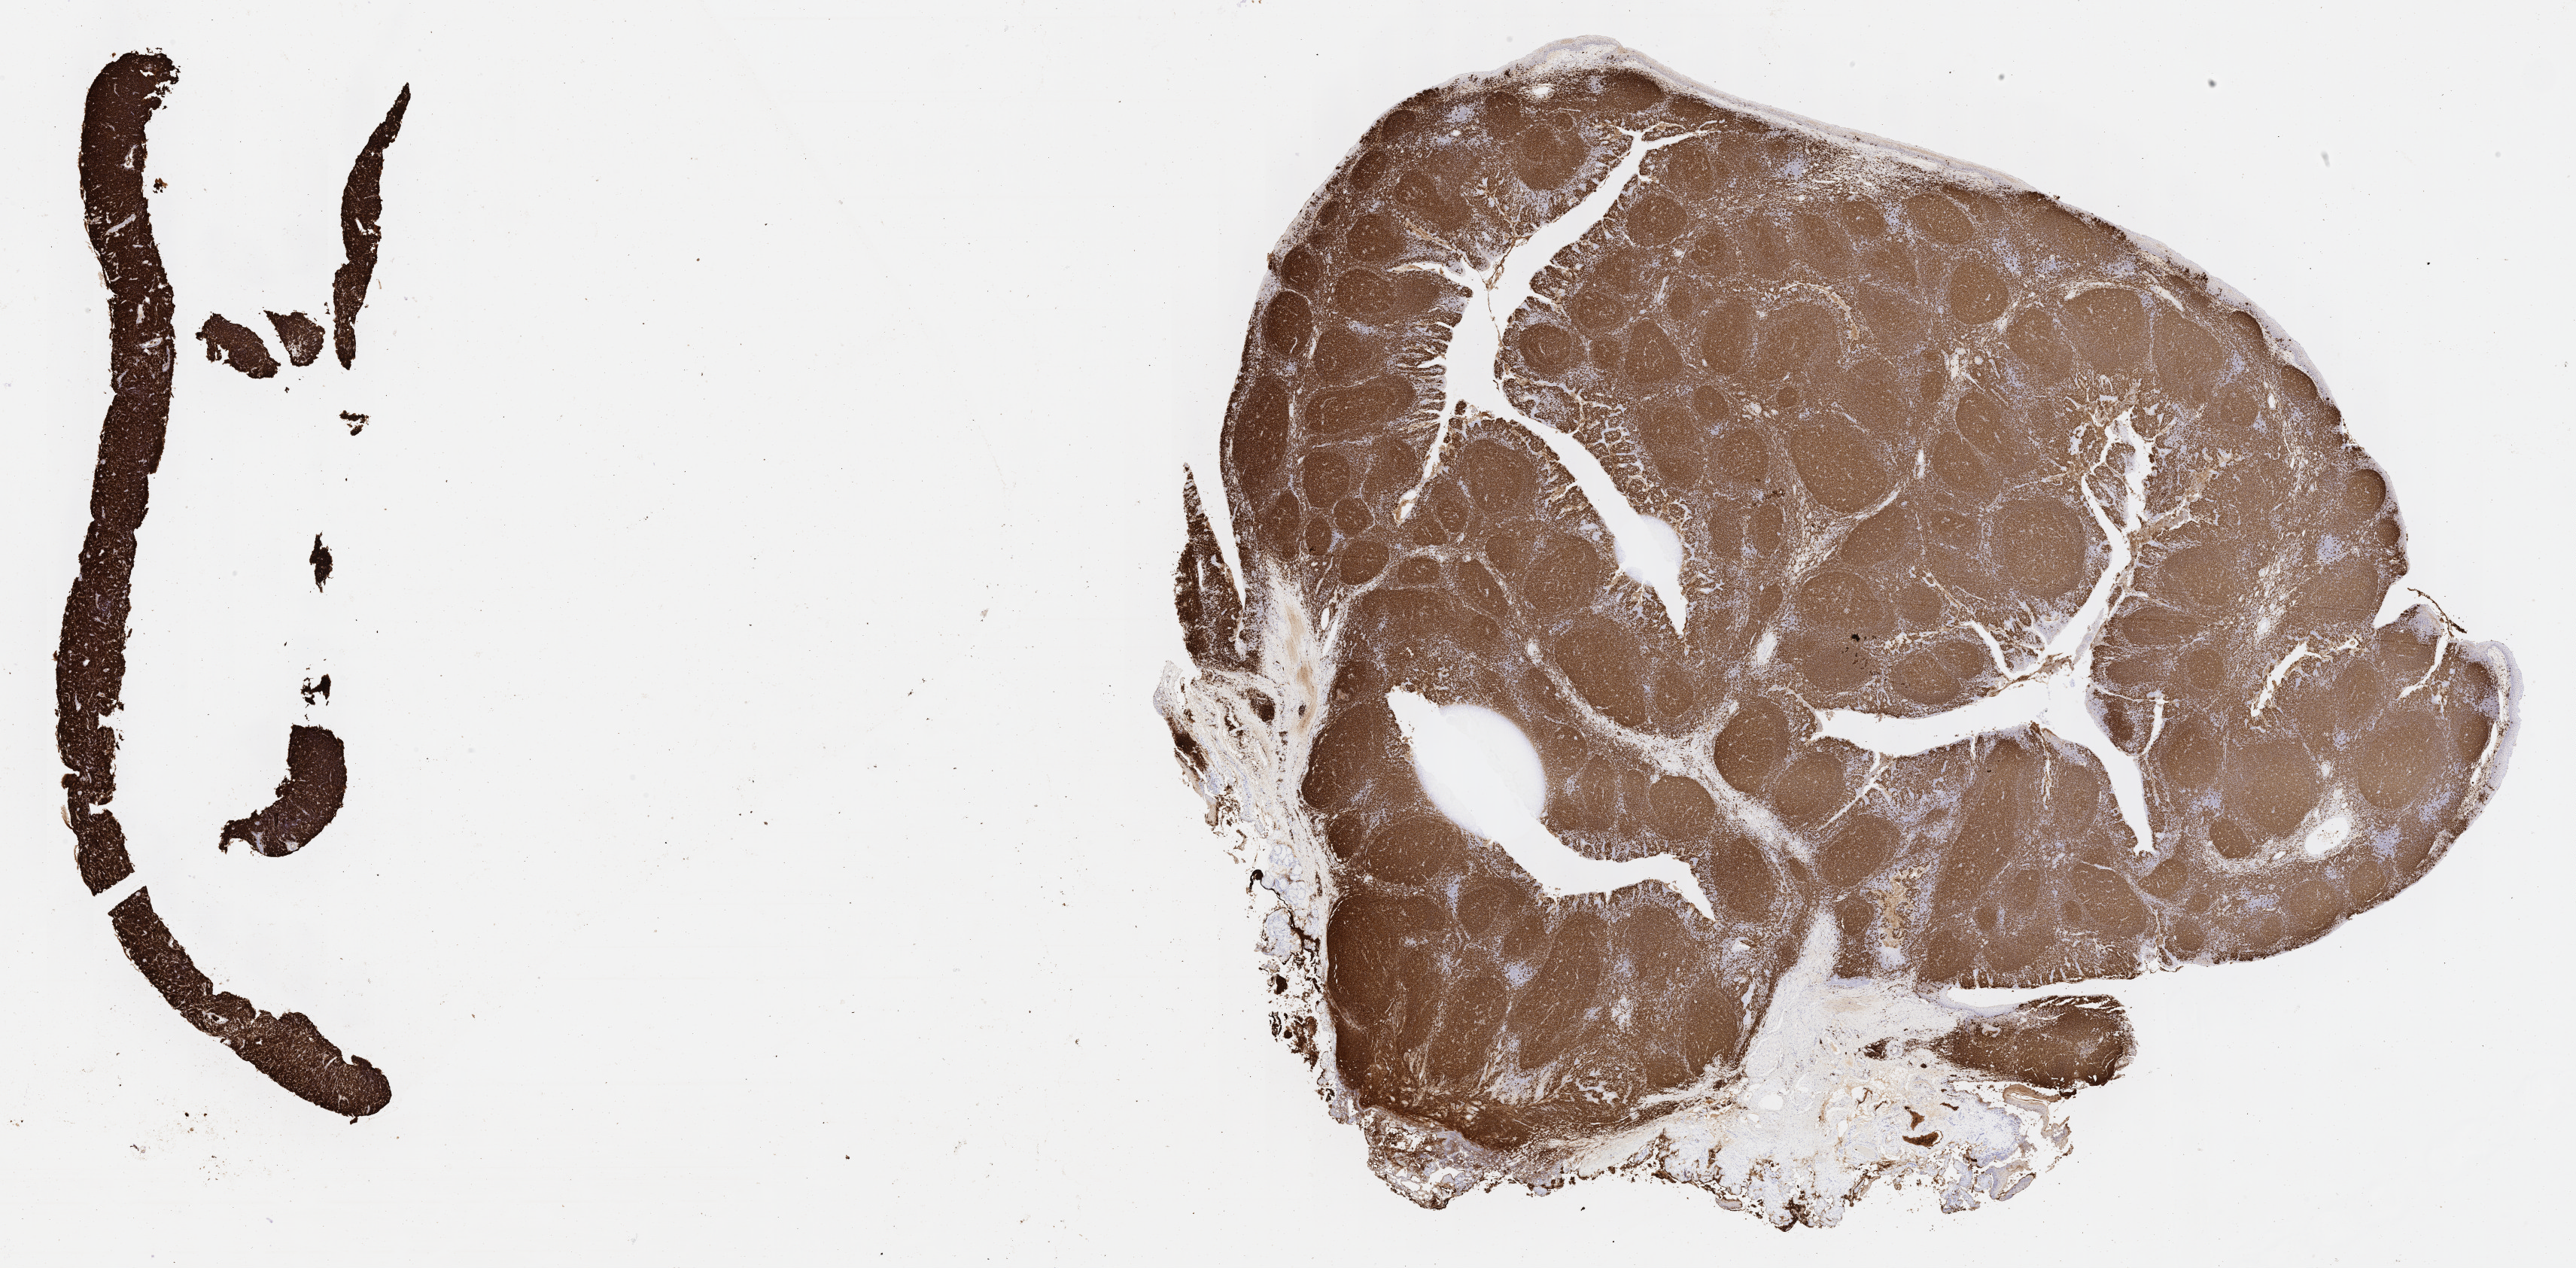
IHC for CD20, whole-slide image — whole scanned area (about 27.7 x 13.6 mm) shown as a low-resolution overview, tumor tissue, site: ovary. Female patient; age at initial diagnosis 9 years.
- diagnosis: Burkitt lymphoma, NOS